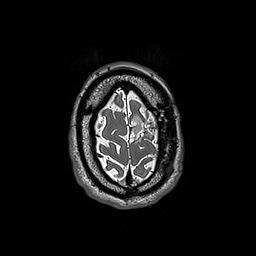
Brain MRI from a brain-tumour surgery series, one axial slice; 1 mm slice thickness; 256 × 256 image matrix, field of view 250 × 250 mm. From the clinical record (not read from this slice): histopathology: Oligodendroglioma; WHO grade: 3; IDH mutation: yes; tumour location: Left Frontal.
Outlined on this slice (expert manual segmentation):
- tumour: bounding box <132,116,146,135> (left, top, right, bottom; pixels)